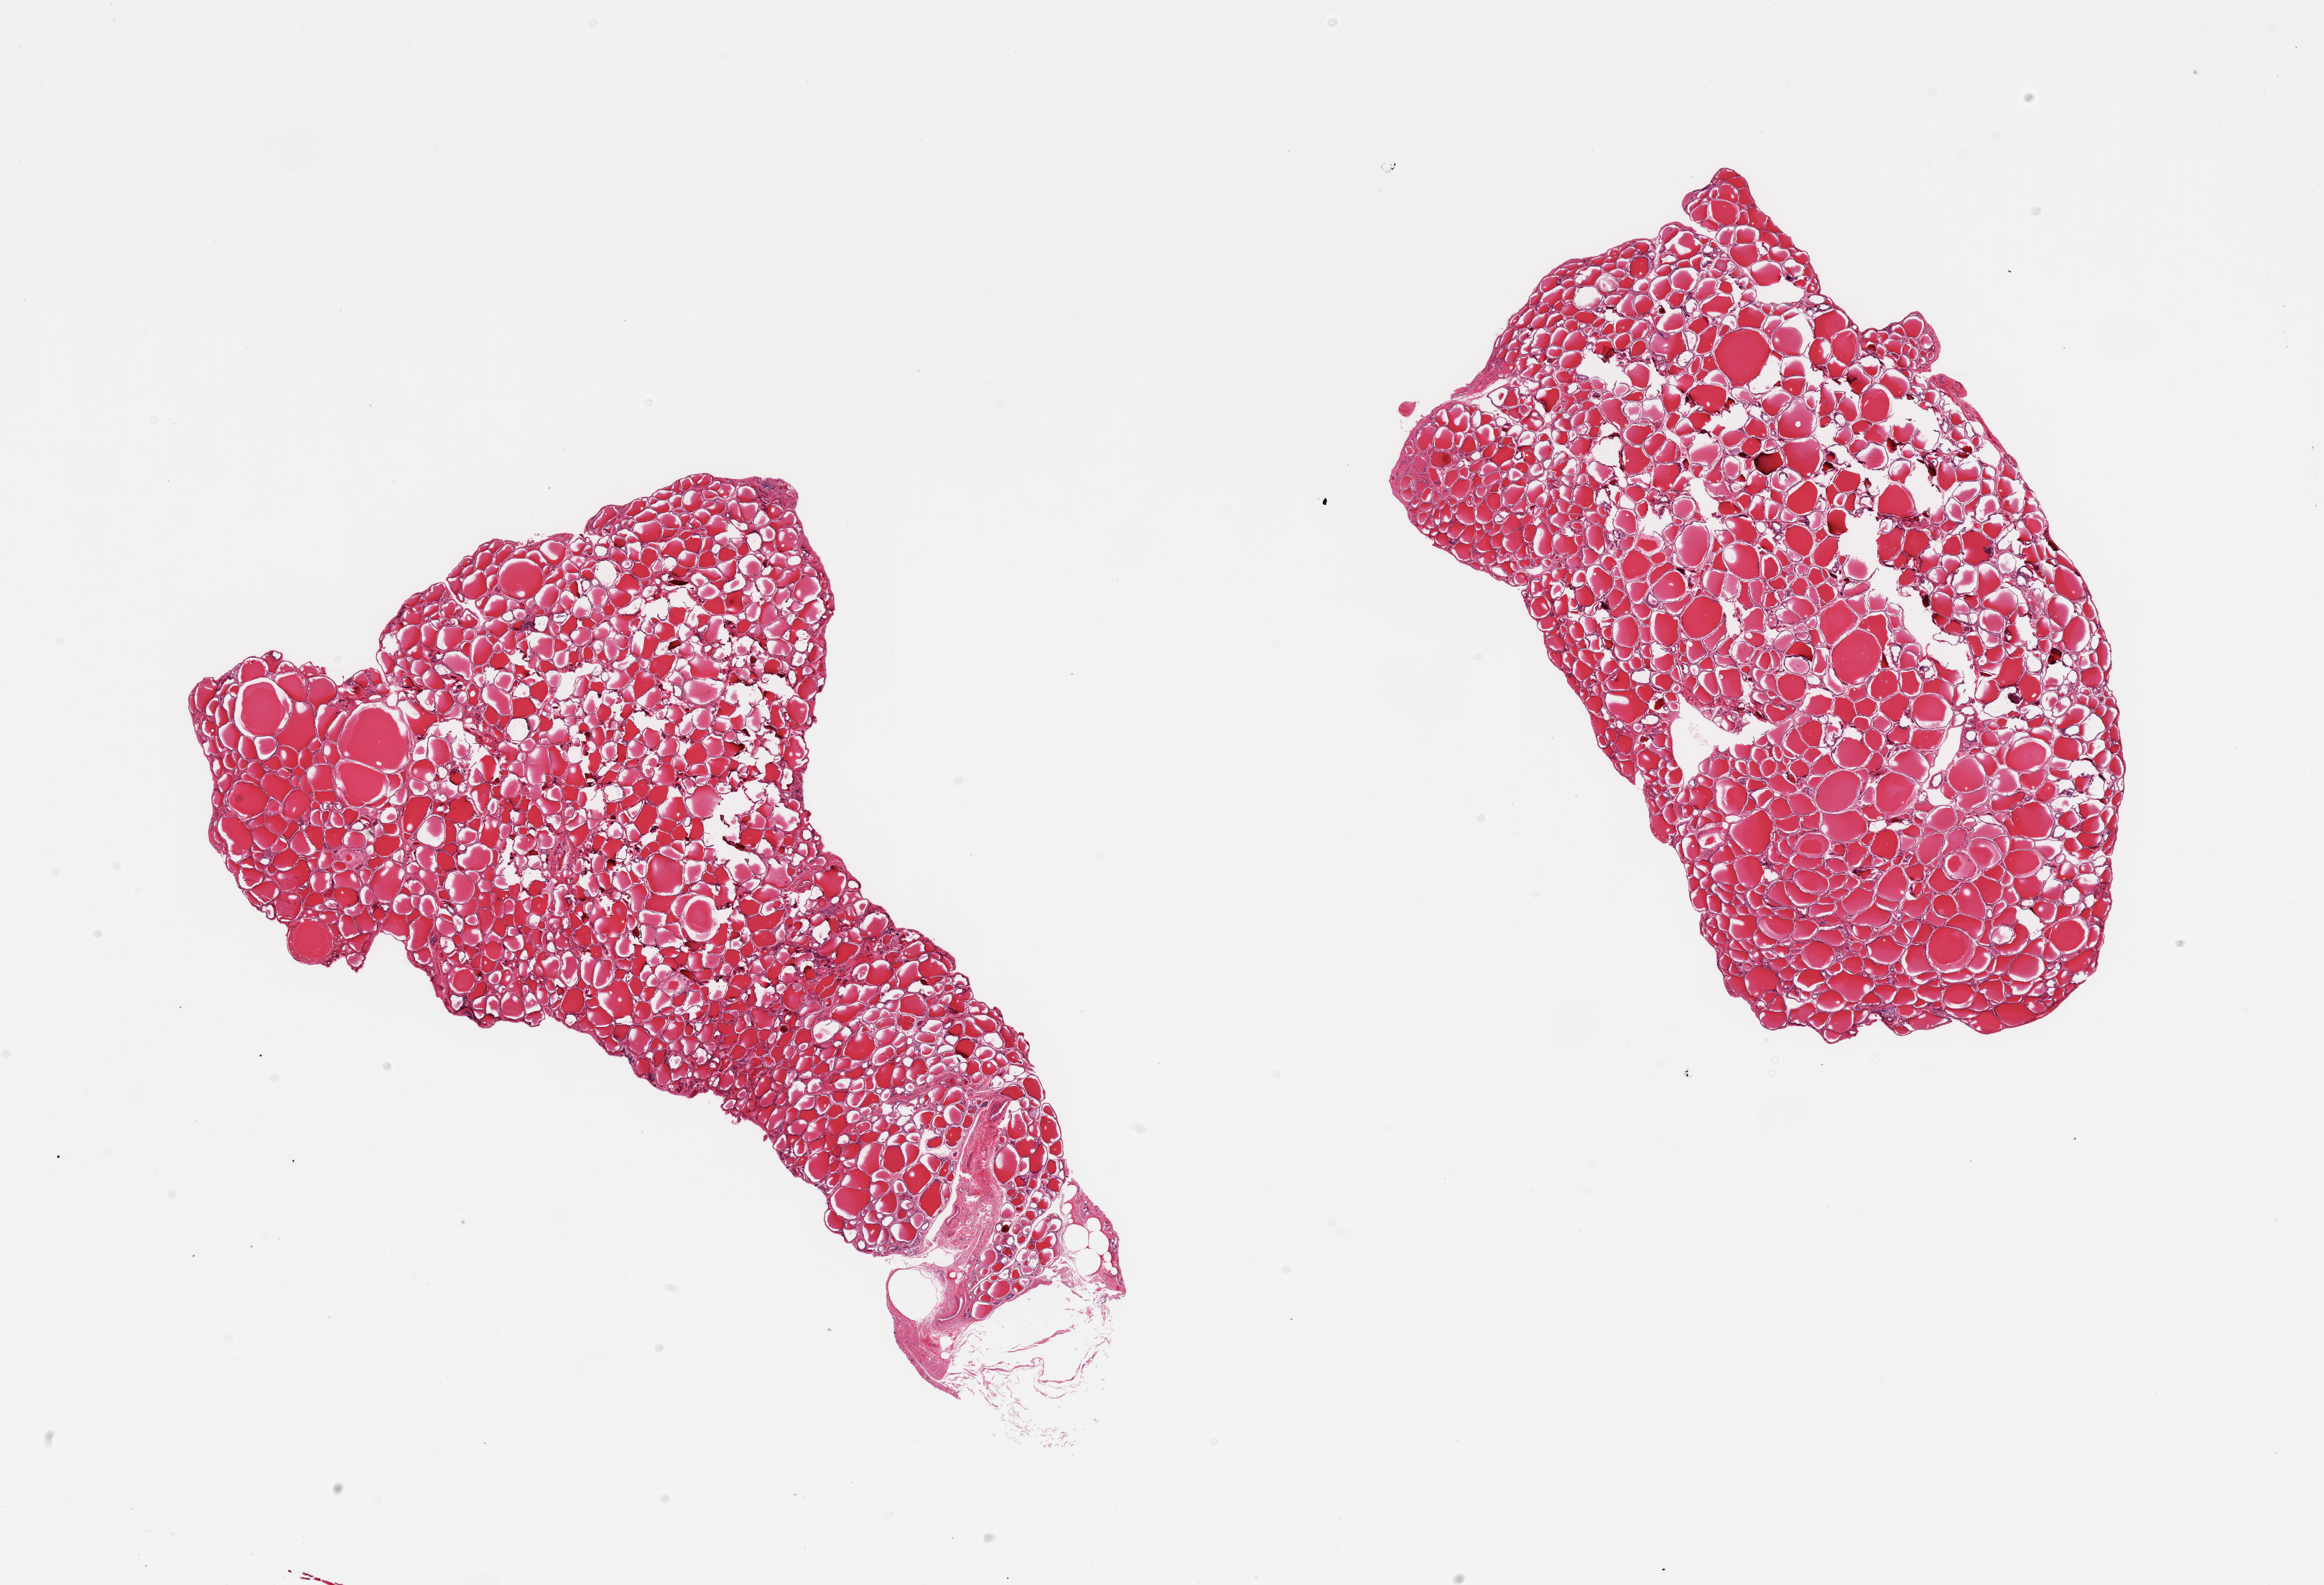
Digitized H&E-stained section, shown as a low-resolution overview of the whole scanned area (about 25.6 x 17.5 mm); PAXgene-fixed paraffin-embedded (PFPE) section; section of thyroid (target tissue); donor tissue sample. Donor: male.
Reviewer comment on this tissue sample: 2 pieces; mild to moderate autolysis.